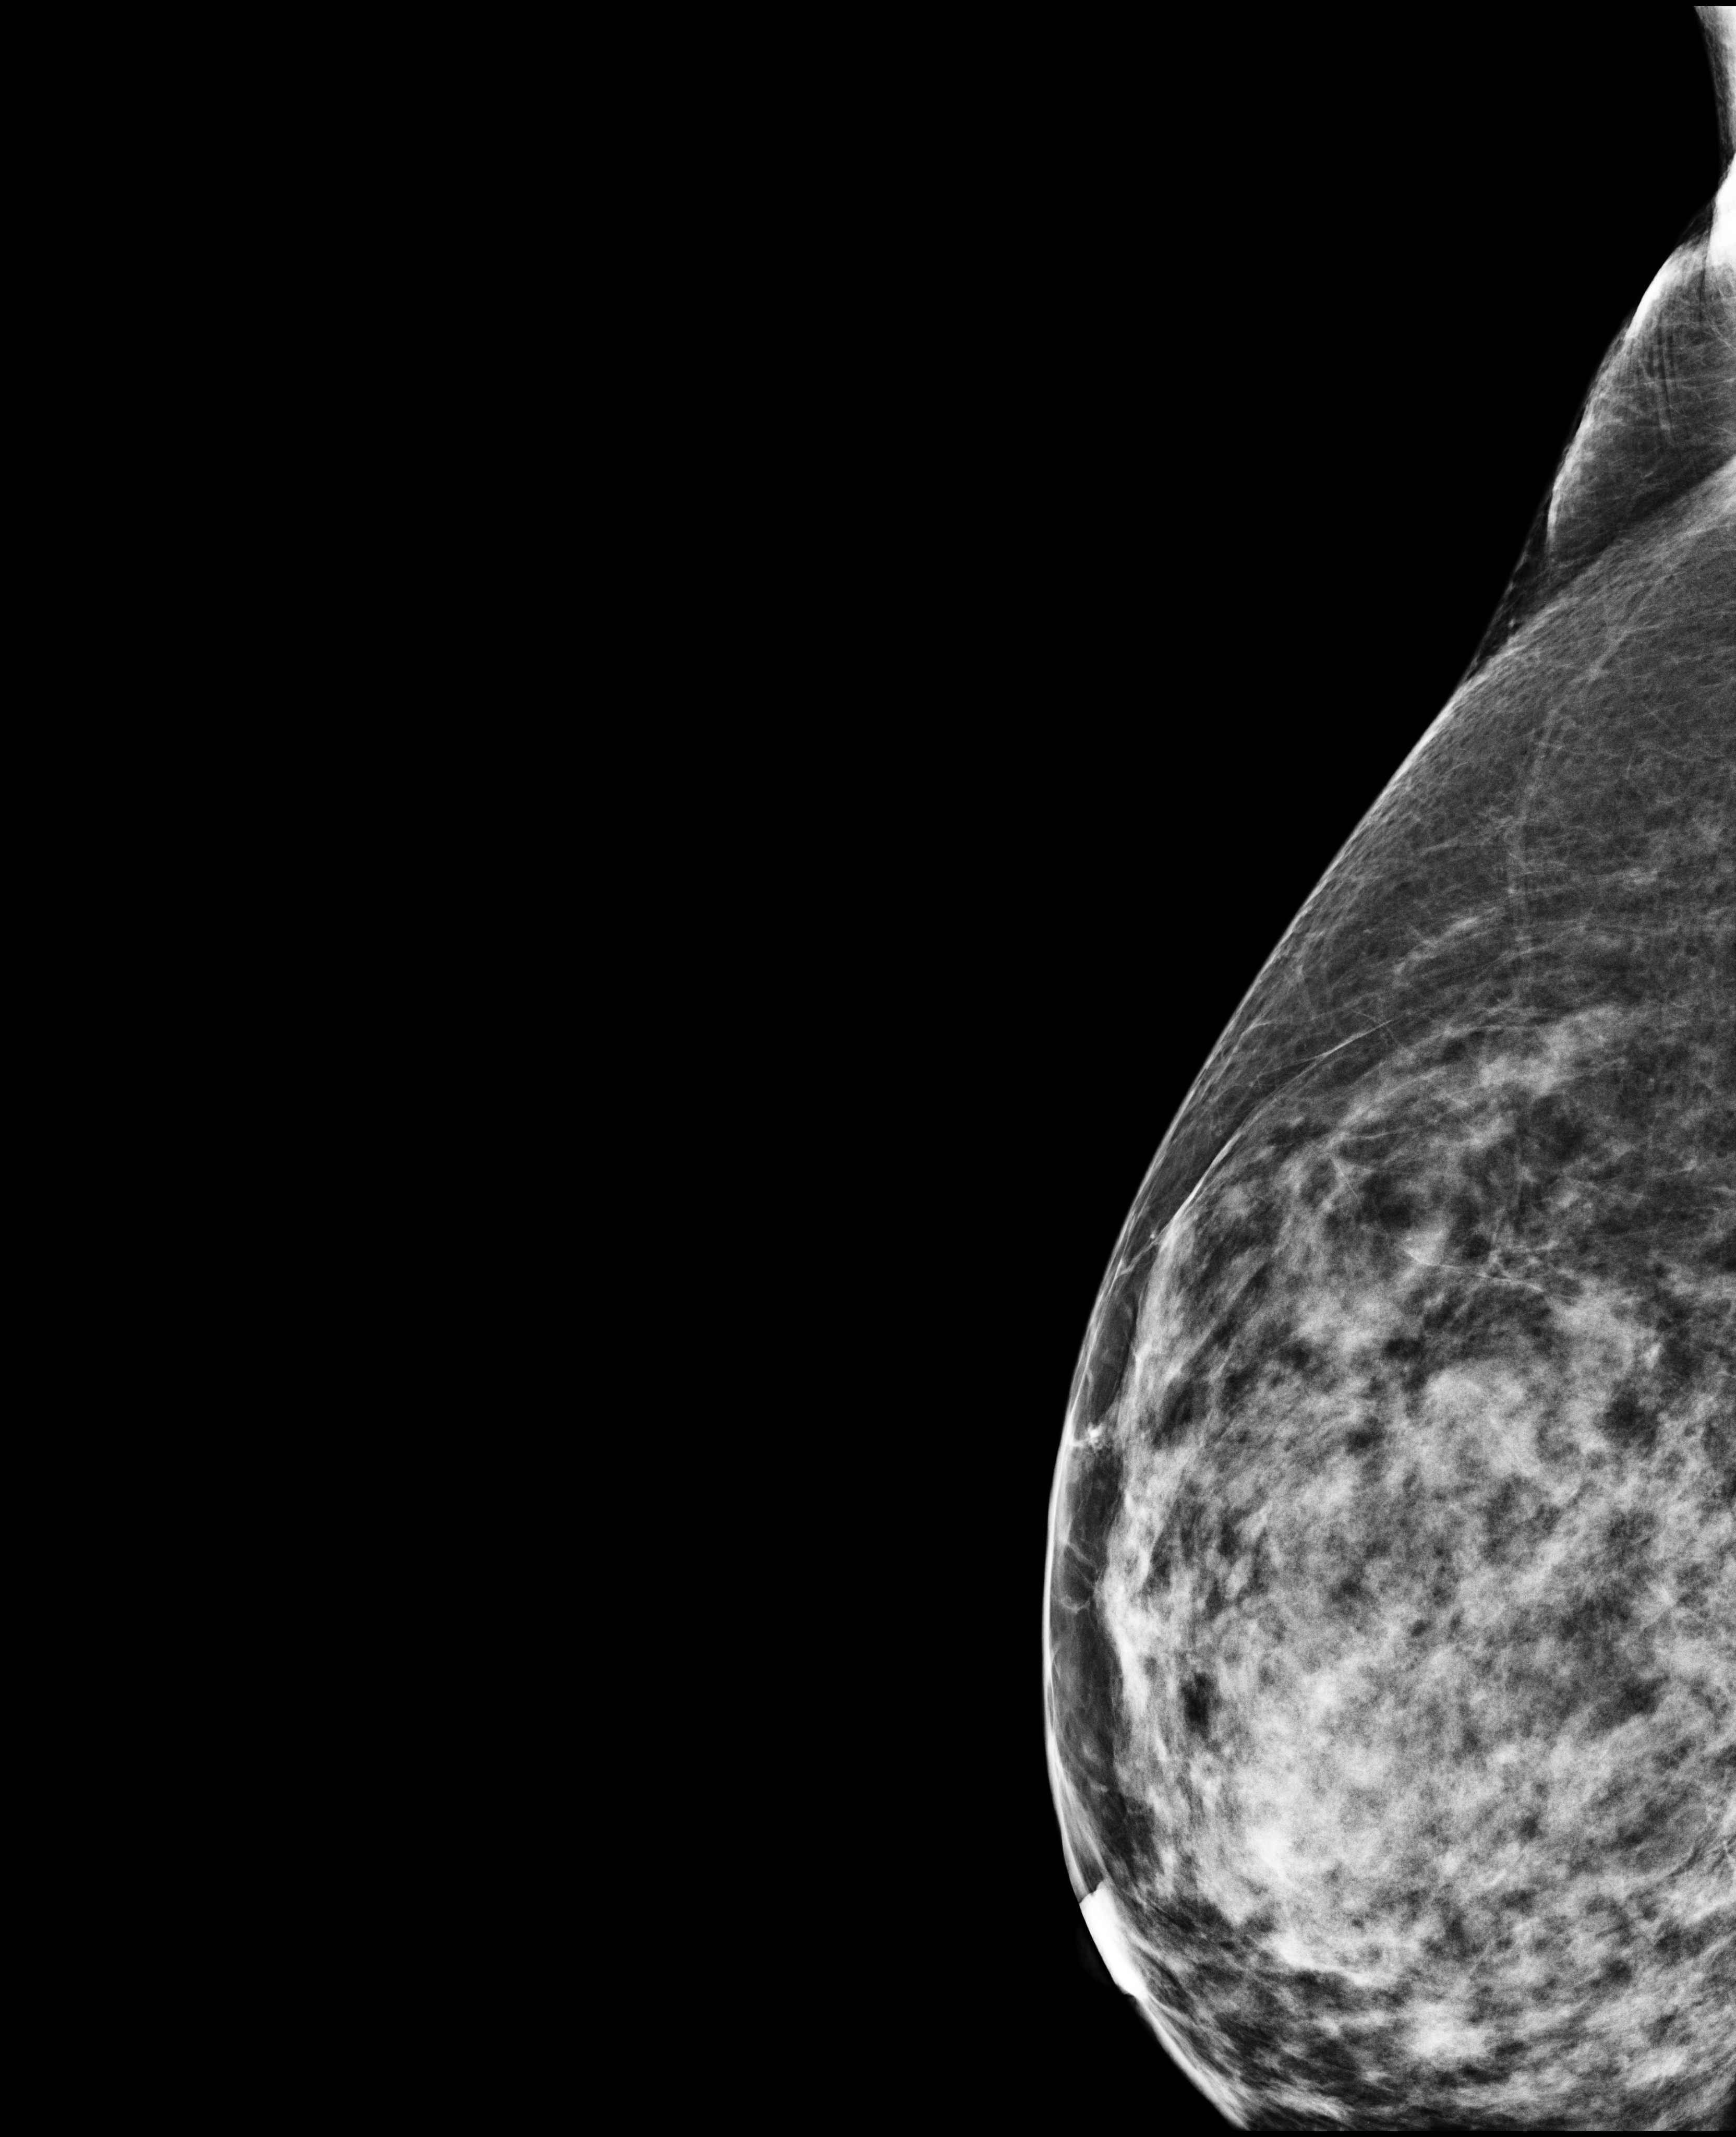
Screening examination; system: Selenia Dimensions. Female patient, age 45 years.
Image type: full-field digital mammogram. Breast: right. Projection: exaggerated CC view (lateral).